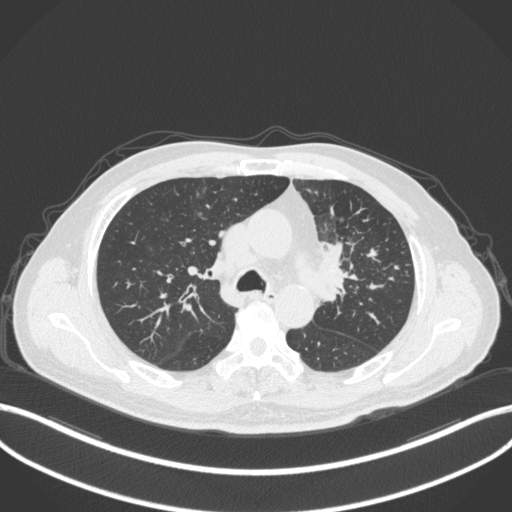
Chest CT, one axial slice; reconstruction kernel B31f; 120 kVp; lung window (W 1500 / L -600 HU); 1 mm slice thickness; 512 × 512 image matrix, field of view 400 × 400 mm. Patient: male, 69 years. From the clinical record (not read from this slice): clinical TNM (as recorded): T2a N2 M0; histopathological grade: G2-3.
Outlined on this slice (rectangle marked by the reading radiologist):
- lung tumour (recorded histology: adenocarcinoma): box from (x=315, y=232) to (x=355, y=307) px